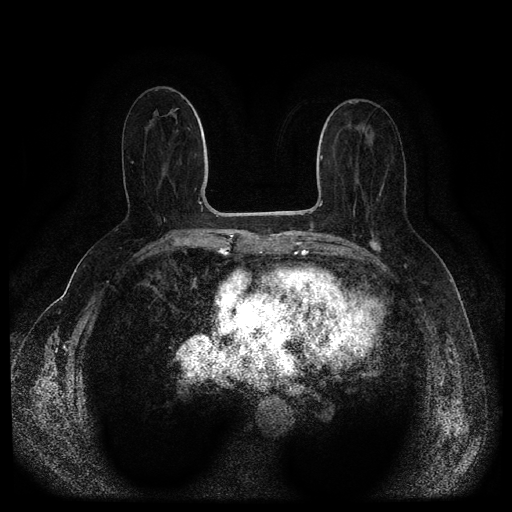
Breast MRI (dynamic contrast-enhanced, multi-phase), one axial slice. Position 46 of 116 along the scan axis. Dynamic contrast-enhanced series, time point 2 of 5 at this slice position (early post-contrast). 1.5 T. TE 2.6 ms, TR 5.4 ms. 2 mm slice thickness. 512 × 512 image matrix, field of view 340 × 340 mm. Patient: female, 67 years.
Annotated regions visible in this slice (semi-automatically segmented with operator editing):
- breast lesion (labelled 'tumour' in the annotation; benign lesions carry a separate 'benign' label): bounding box (x1, y1, x2, y2) in pixels: (369, 239, 383, 254)